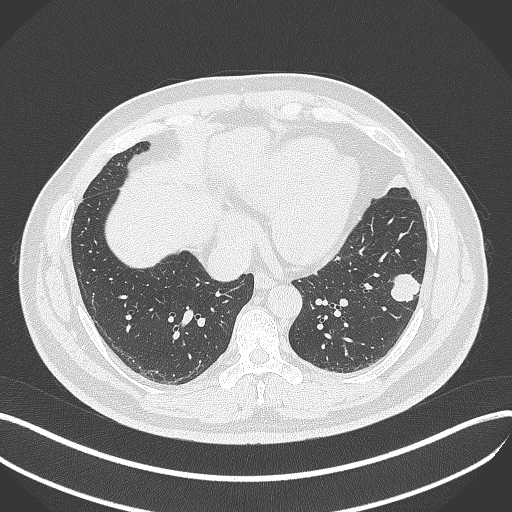
Chest CT, one axial slice. Slice 142 of 429 in the series (ordered by position). 120 kVp. Lung window (W 1500 / L -600 HU). 1 mm slice thickness. 512 × 512 image matrix, field of view 400 × 400 mm. Male patient, age 39 years. Case-level facts recorded for this patient, not image findings: clinical TNM (as recorded): T2a N0 M0; histopathological grade: G2-3.
Annotated regions visible in this slice (bounding box drawn by a radiologist):
- lung tumour (recorded histology: adenocarcinoma): bounding box (x1, y1, x2, y2) in pixels: (386, 271, 423, 308)